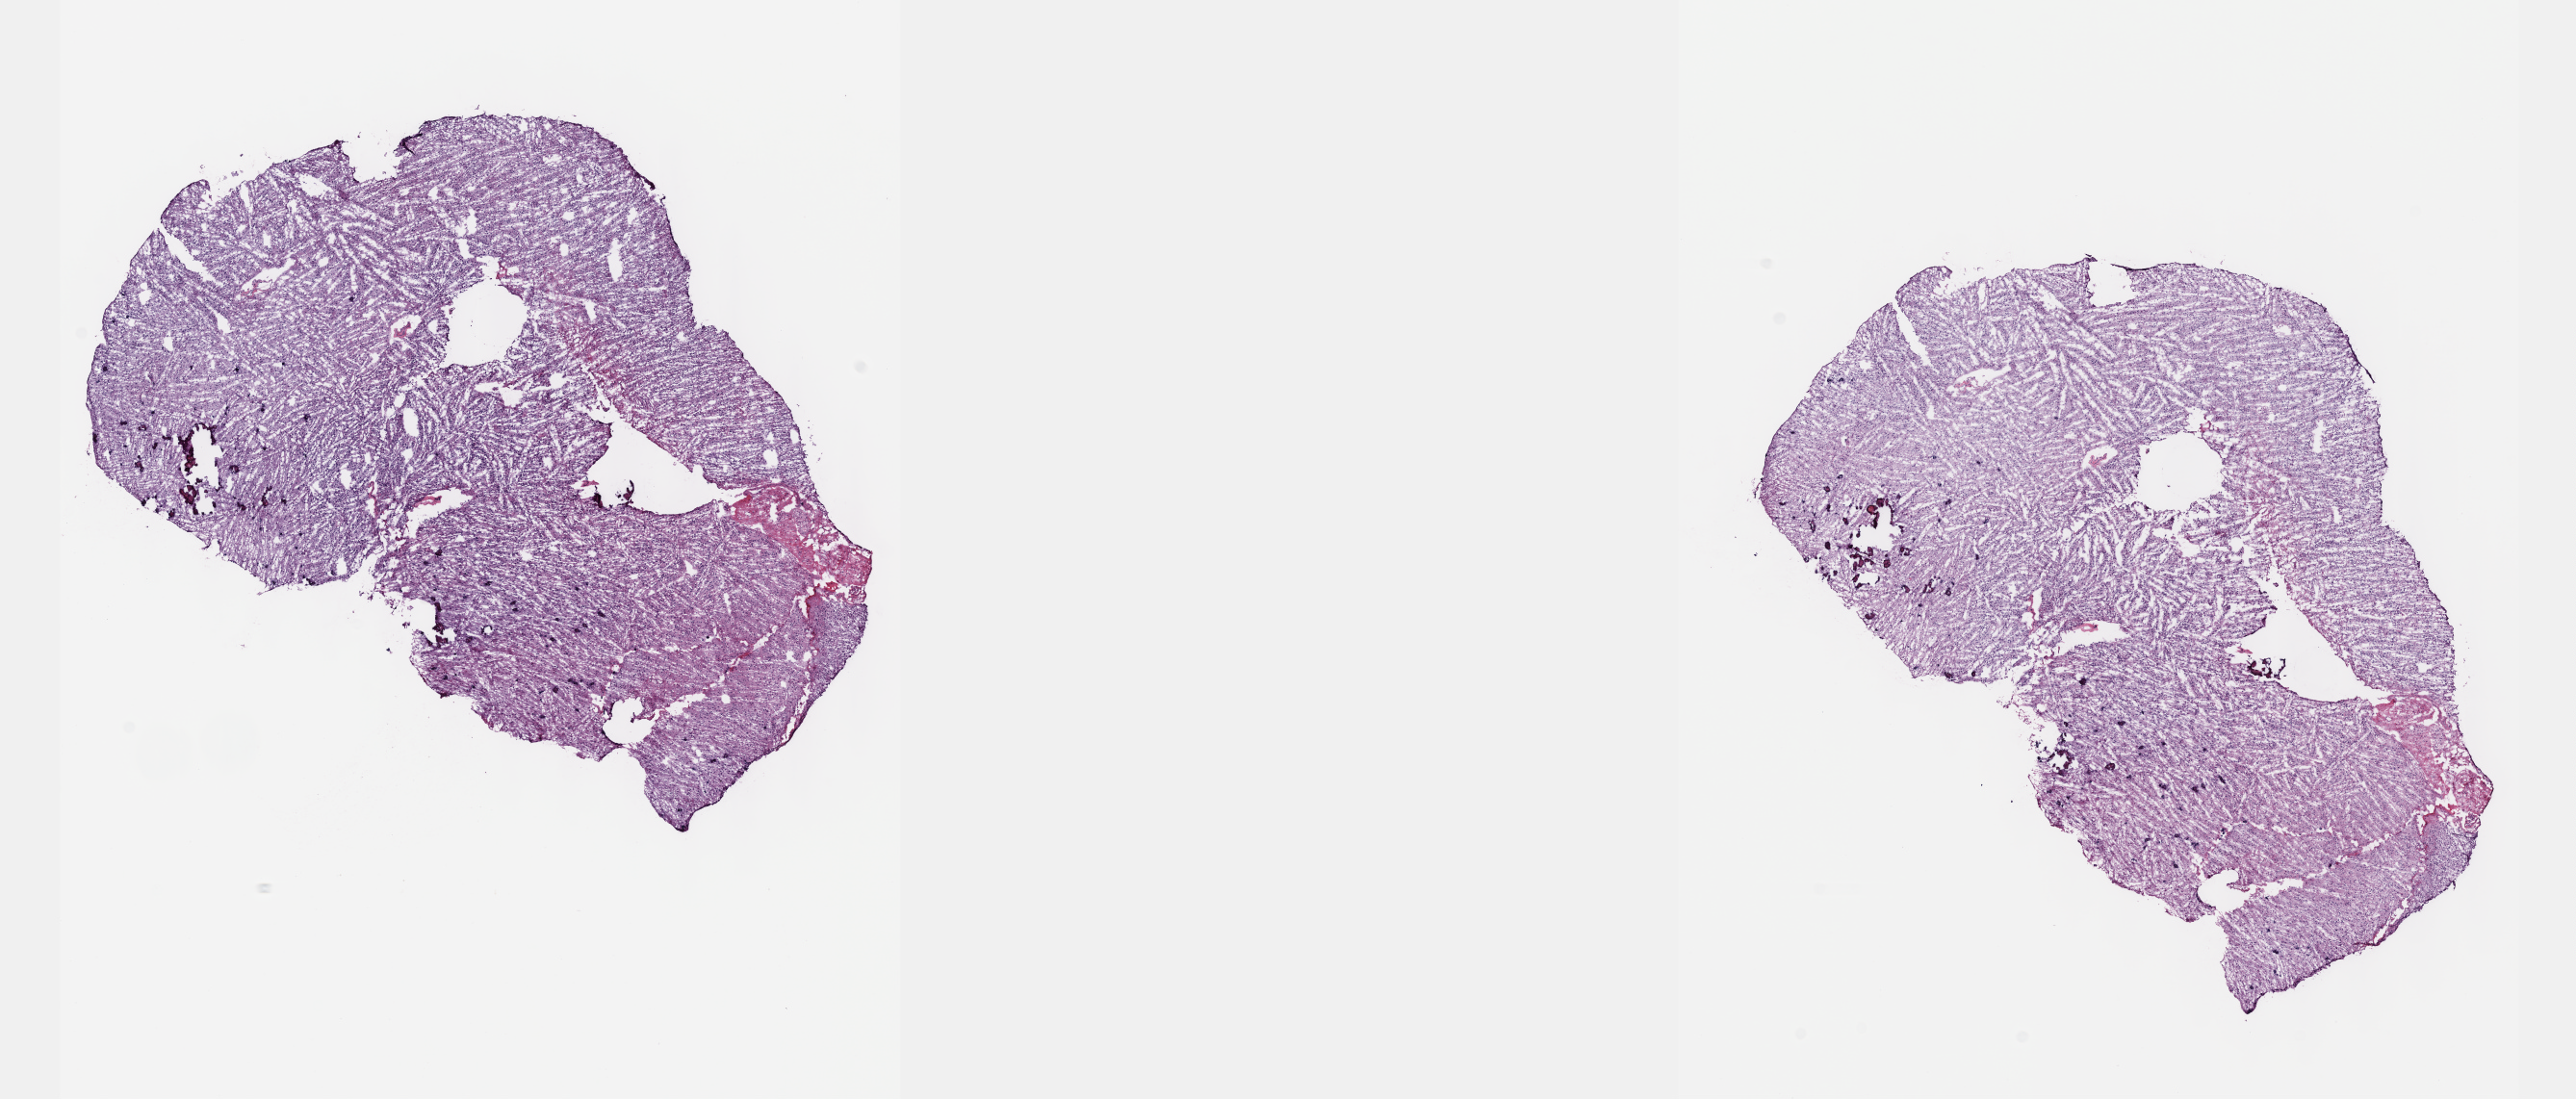
Whole-slide histology image, H&E, a low-resolution overview of the entire scanned area, about 21.6 x 9.2 mm. Frozen section. Brain, primary tumour sample. Male patient; age at initial diagnosis 32 years. Pathologist review of this section (percent, as recorded): tumour cells 50%, tumour nuclei 90%.
Histologic diagnosis: Oligodendroglioma, NOS (cerebrum).